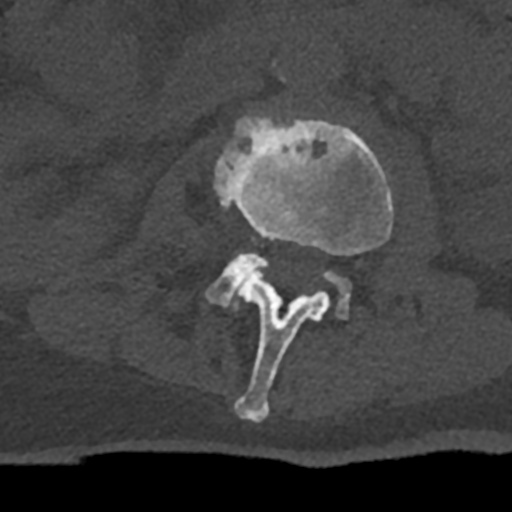
CT including the spine, one axial slice; slice 359 of 797 in the series (ordered by position); reconstruction kernel Br40s/3; bone window (W 1800 / L 400 HU); 512 × 512 image matrix, field of view 160 × 160 mm. Patient: male, 74 years. Case-level facts recorded for this patient, not image findings: primary cancer: renal.
Outlined on this slice (semi-automatic segmentation, software-assisted and operator-edited):
- L2 vertebra: bounding box [x1, y1, x2, y2] px = [214, 114, 394, 421]
- L3 vertebra: [207, 252, 351, 319]